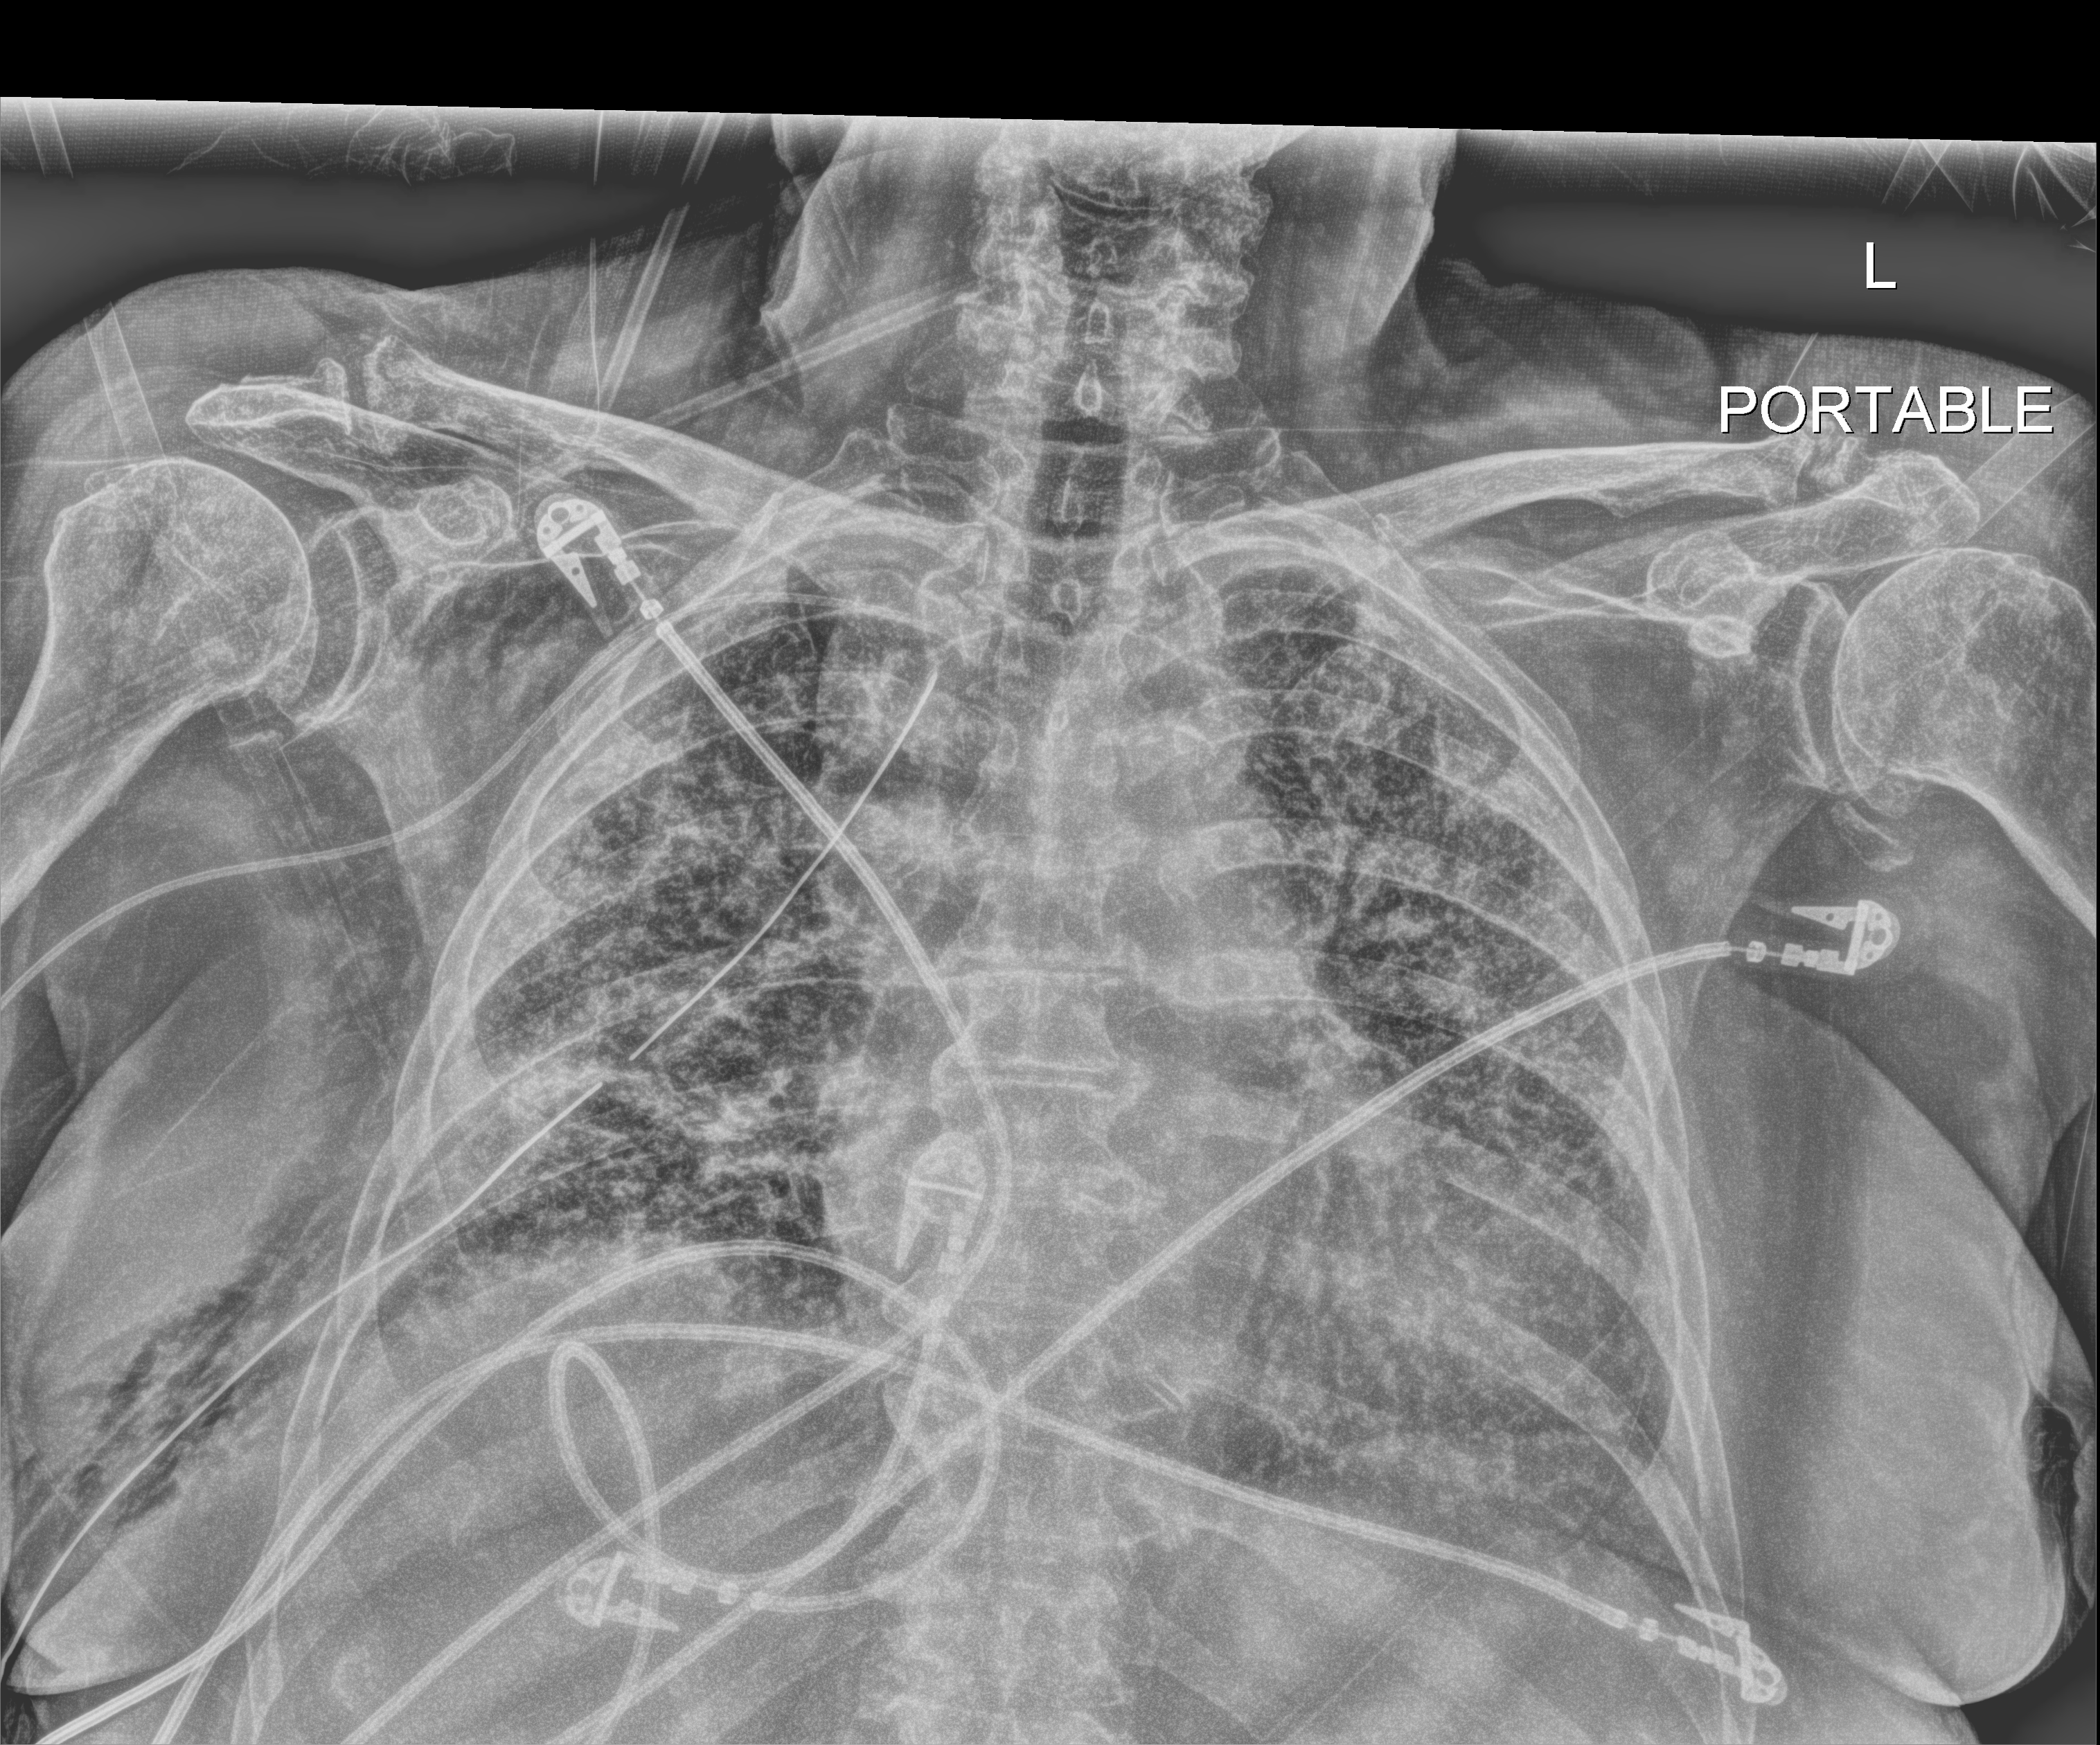
Bedside chest radiograph (digital radiography), anteroposterior (AP) projection. Female patient hospitalised with COVID-19, age 75–90 years.
Hospital-stay facts (about this admission, not read from this image; timing relative to this image not recorded): hypertension (admission record): no; chronic kidney disease (admission record): no.